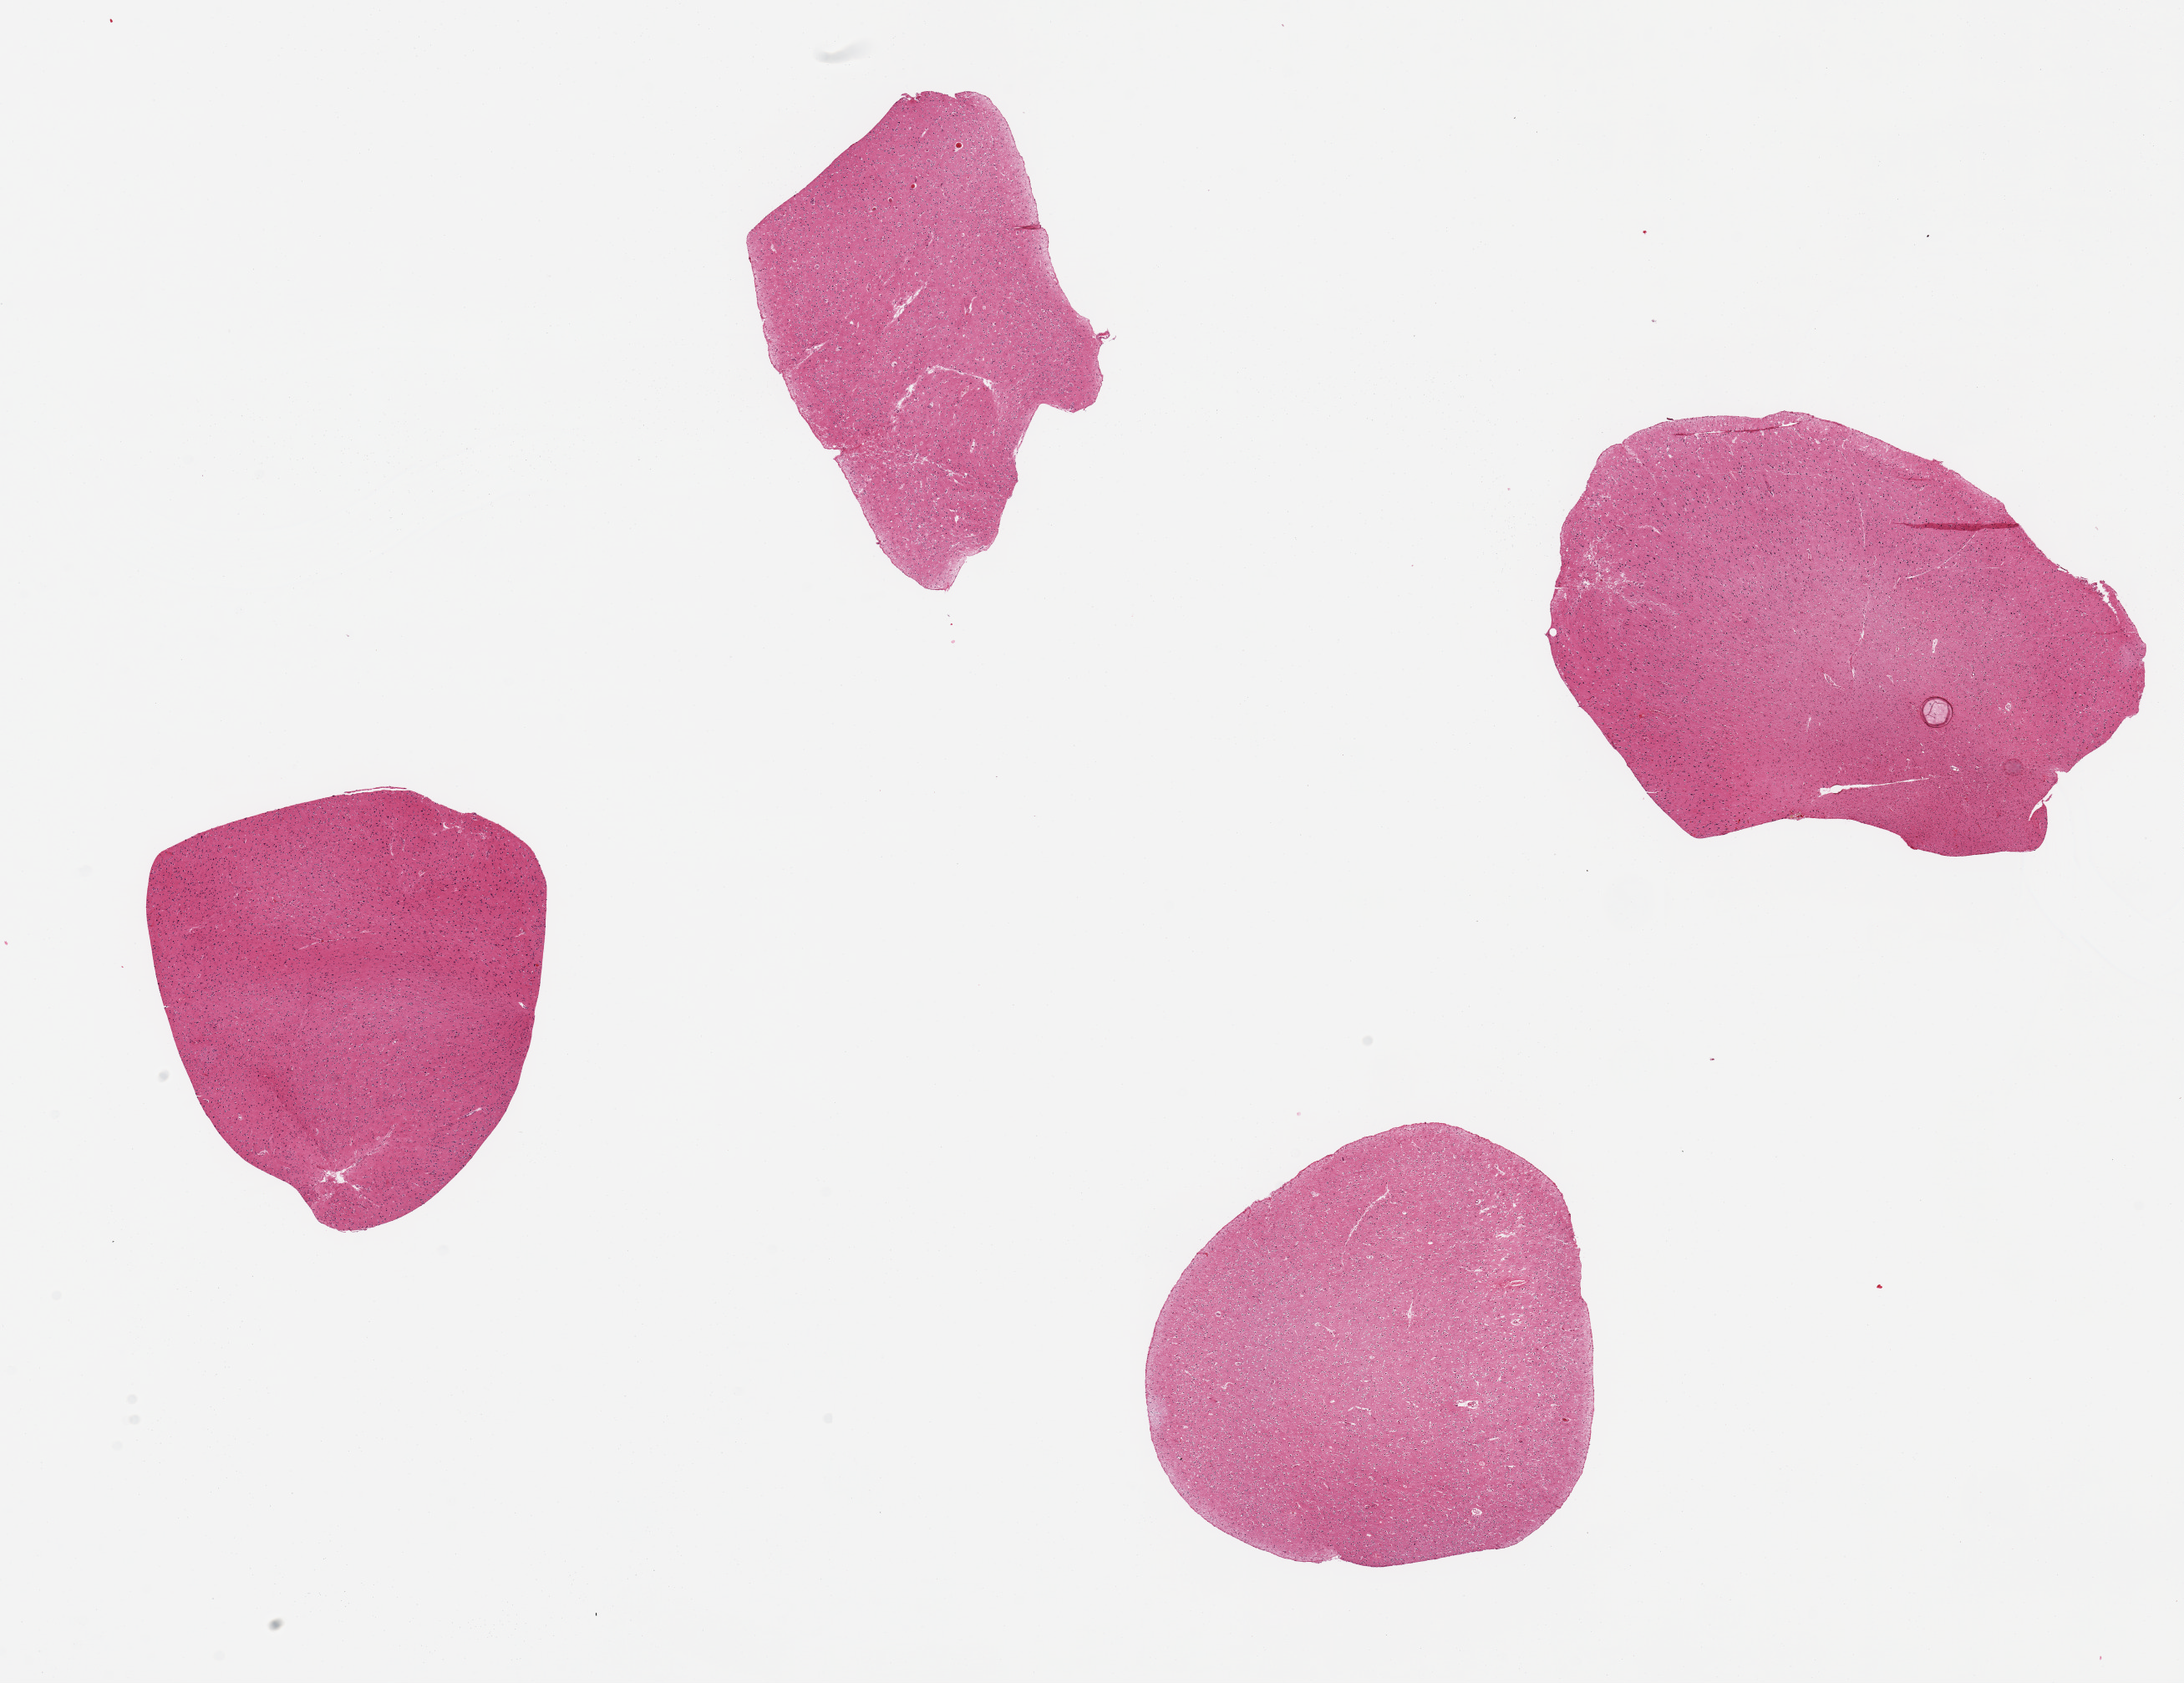
H&E whole-slide image — a low-resolution overview of the entire scanned area, about 20.7 x 15.9 mm, PAXgene-fixed, paraffin-embedded tissue, section of cerebral cortex (target tissue), tissue donor sample. Donor: female.
Review note (as recorded): 4 pieces, no abnormalities.